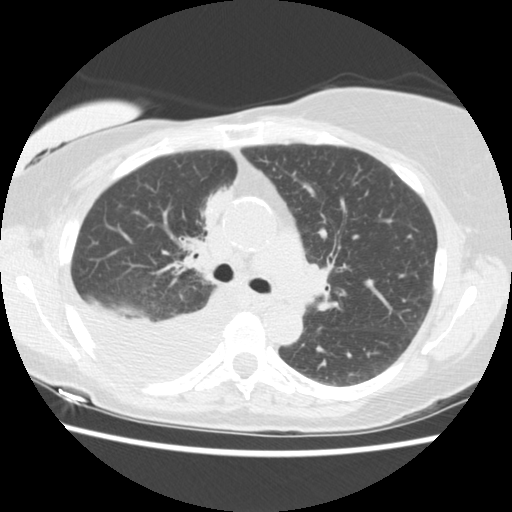
Chest CT (low-dose screening protocol), one axial image. Third annual screen. Lung window (W 1500 / L -600 HU). Standard (soft-tissue) reconstruction kernel (STANDARD). Slice 62 of 157 in the series. 512 × 512 image matrix. Female participant, aged 56 years at enrolment.
Expert-annotated lung lesion, bounding box [x1, y1, x2, y2] px = [182, 182, 243, 248]. The screening reader recorded 2 non-calcified nodules or masses ≥4 mm on this exam (right middle lobe, right lower lobe); which of them this box marks is not recorded.